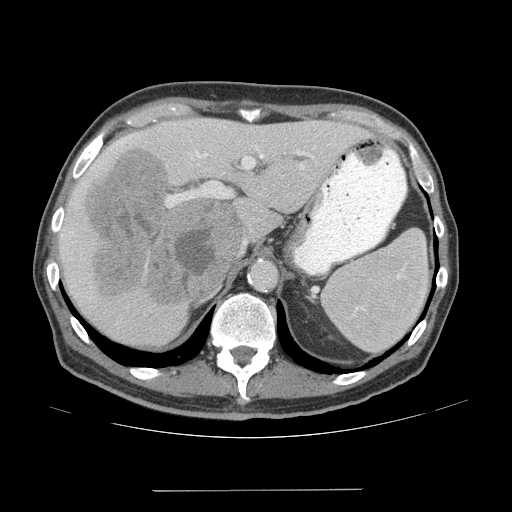
Contrast-enhanced abdominal CT (liver protocol), one axial slice. Position 44 of 77 along the scan axis. 140 kVp. Soft-tissue window (W 400 / L 40 HU). 2.5 mm slice thickness. 512 × 512 image matrix, field of view 400 × 400 mm. Case-level facts recorded for this patient, not image findings: diagnosis: hepatocellular carcinoma (patient treated with transarterial chemoembolisation; whether this scan precedes or follows treatment is not stated here); TNM stage (as recorded): Stage-IVA.
Outlined on this slice (semi-automatic segmentation, software-assisted and operator-edited):
- liver parenchyma outside the tumour (the mass and vessels are separate outlines, so this box may not span the whole liver): bounding box <58,118,370,346> (left, top, right, bottom; pixels)
- mass: <86,149,249,304>
- liver vessels: <62,126,313,237>